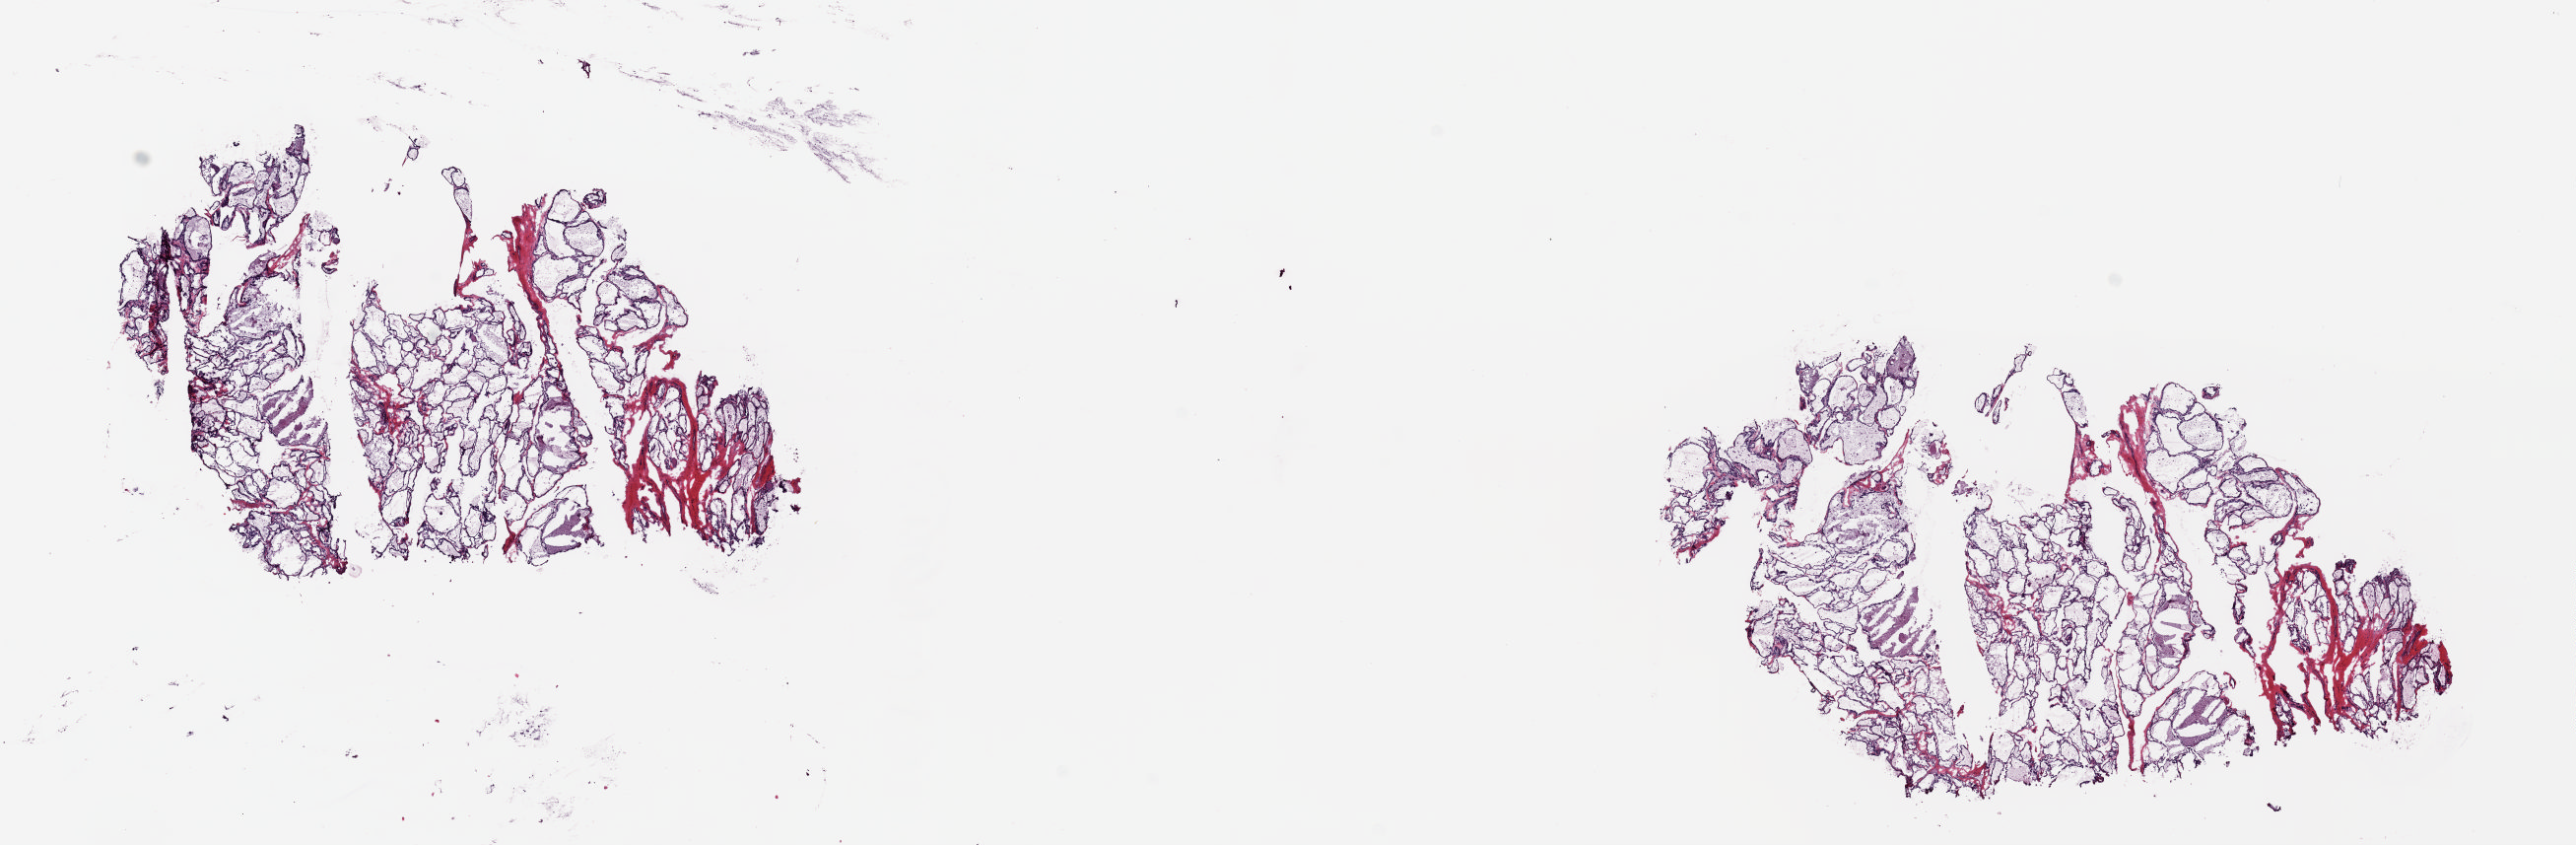
Whole-slide histology image, H&E, whole scanned area (about 20.6 x 6.8 mm, from a 20x scan) shown as a low-resolution overview. Frozen section from the top of the tissue portion. Thyroid, solid tissue normal (non-tumour tissue) sample. Male patient; age at initial diagnosis 35 years. Pathologist review of this section (percent, as recorded): tumour cells 0%, tumour nuclei 0%, normal cells 100%, stromal cells 0%, necrosis 0%. Inflammatory infiltration, as recorded: lymphocyte infiltration 1%, monocyte infiltration 1%, neutrophil infiltration 0%.
This section: solid tissue normal (non-tumour) sample from the same patient. Patient diagnosis: Papillary adenocarcinoma, NOS (thyroid gland).